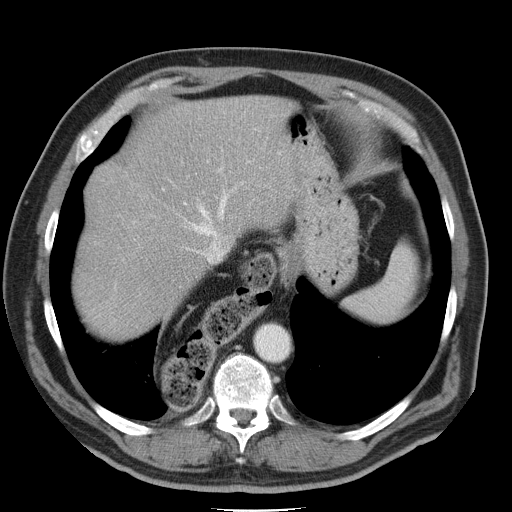
Contrast-enhanced abdominal CT, one axial slice. Slice 38 of 45 in the series (ordered by position). 120 kVp. Intravenous contrast given. Soft-tissue window (W 400 / L 40 HU). 512 × 512 image matrix, field of view 386 × 386 mm. Male patient, age 65 years. Case-level facts recorded for this patient, not image findings: diagnosis: colorectal cancer liver metastases, imaged before liver resection; multiple liver metastases: yes; largest metastasis: 4.9 cm; chemotherapy before resection: yes.
Outlined on this slice (manually delineated by an expert):
- hepatic veins: bounding box [x1, y1, x2, y2] px = [106, 161, 261, 325]
- liver: [76, 96, 289, 334]
- planned liver remnant (the part of the liver to remain after resection): [118, 96, 289, 245]
- portal vein (with intrahepatic branches): [127, 219, 140, 229]